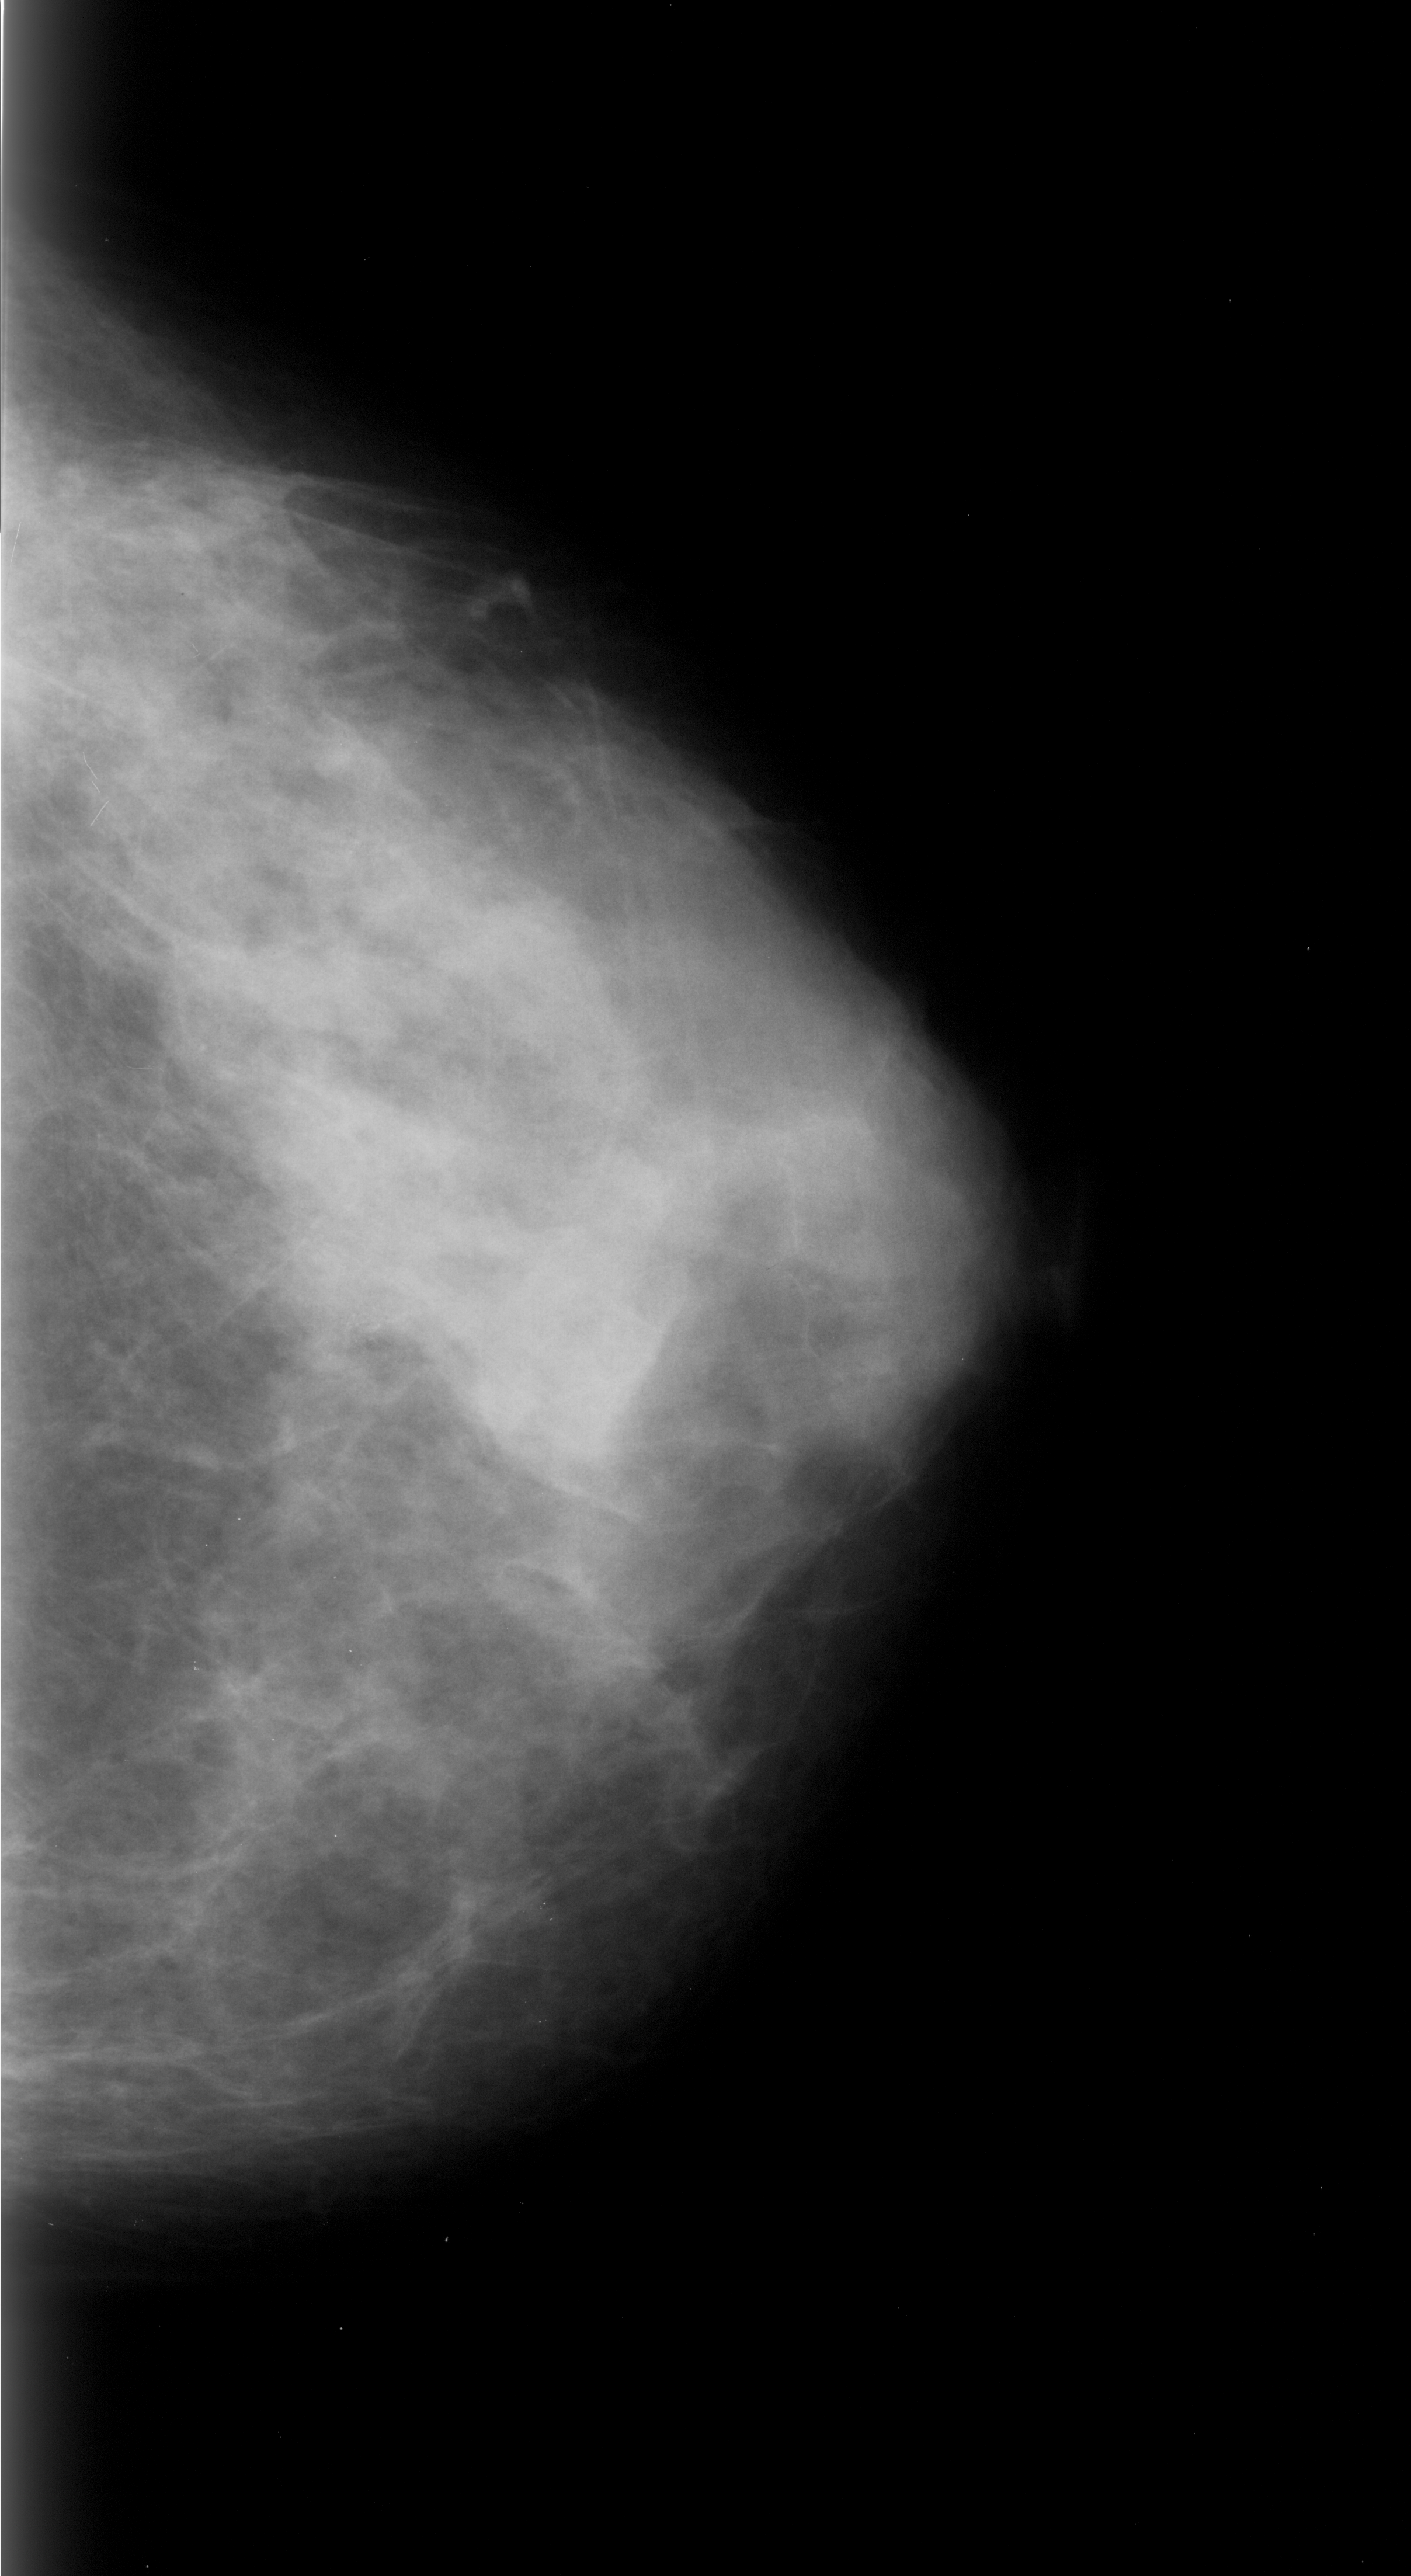
Mammogram (digitized film), right breast, CC view, BI-RADS breast density category 4 (scale 1–4).
- Radiologist-marked abnormalities on this image: calcifications, morphology pleomorphic, distribution clustered; BI-RADS assessment category 4; subtlety rating 1 on a 1 (subtle) to 5 (obvious) scale; pathology result (as recorded, not read from the image): malignant.